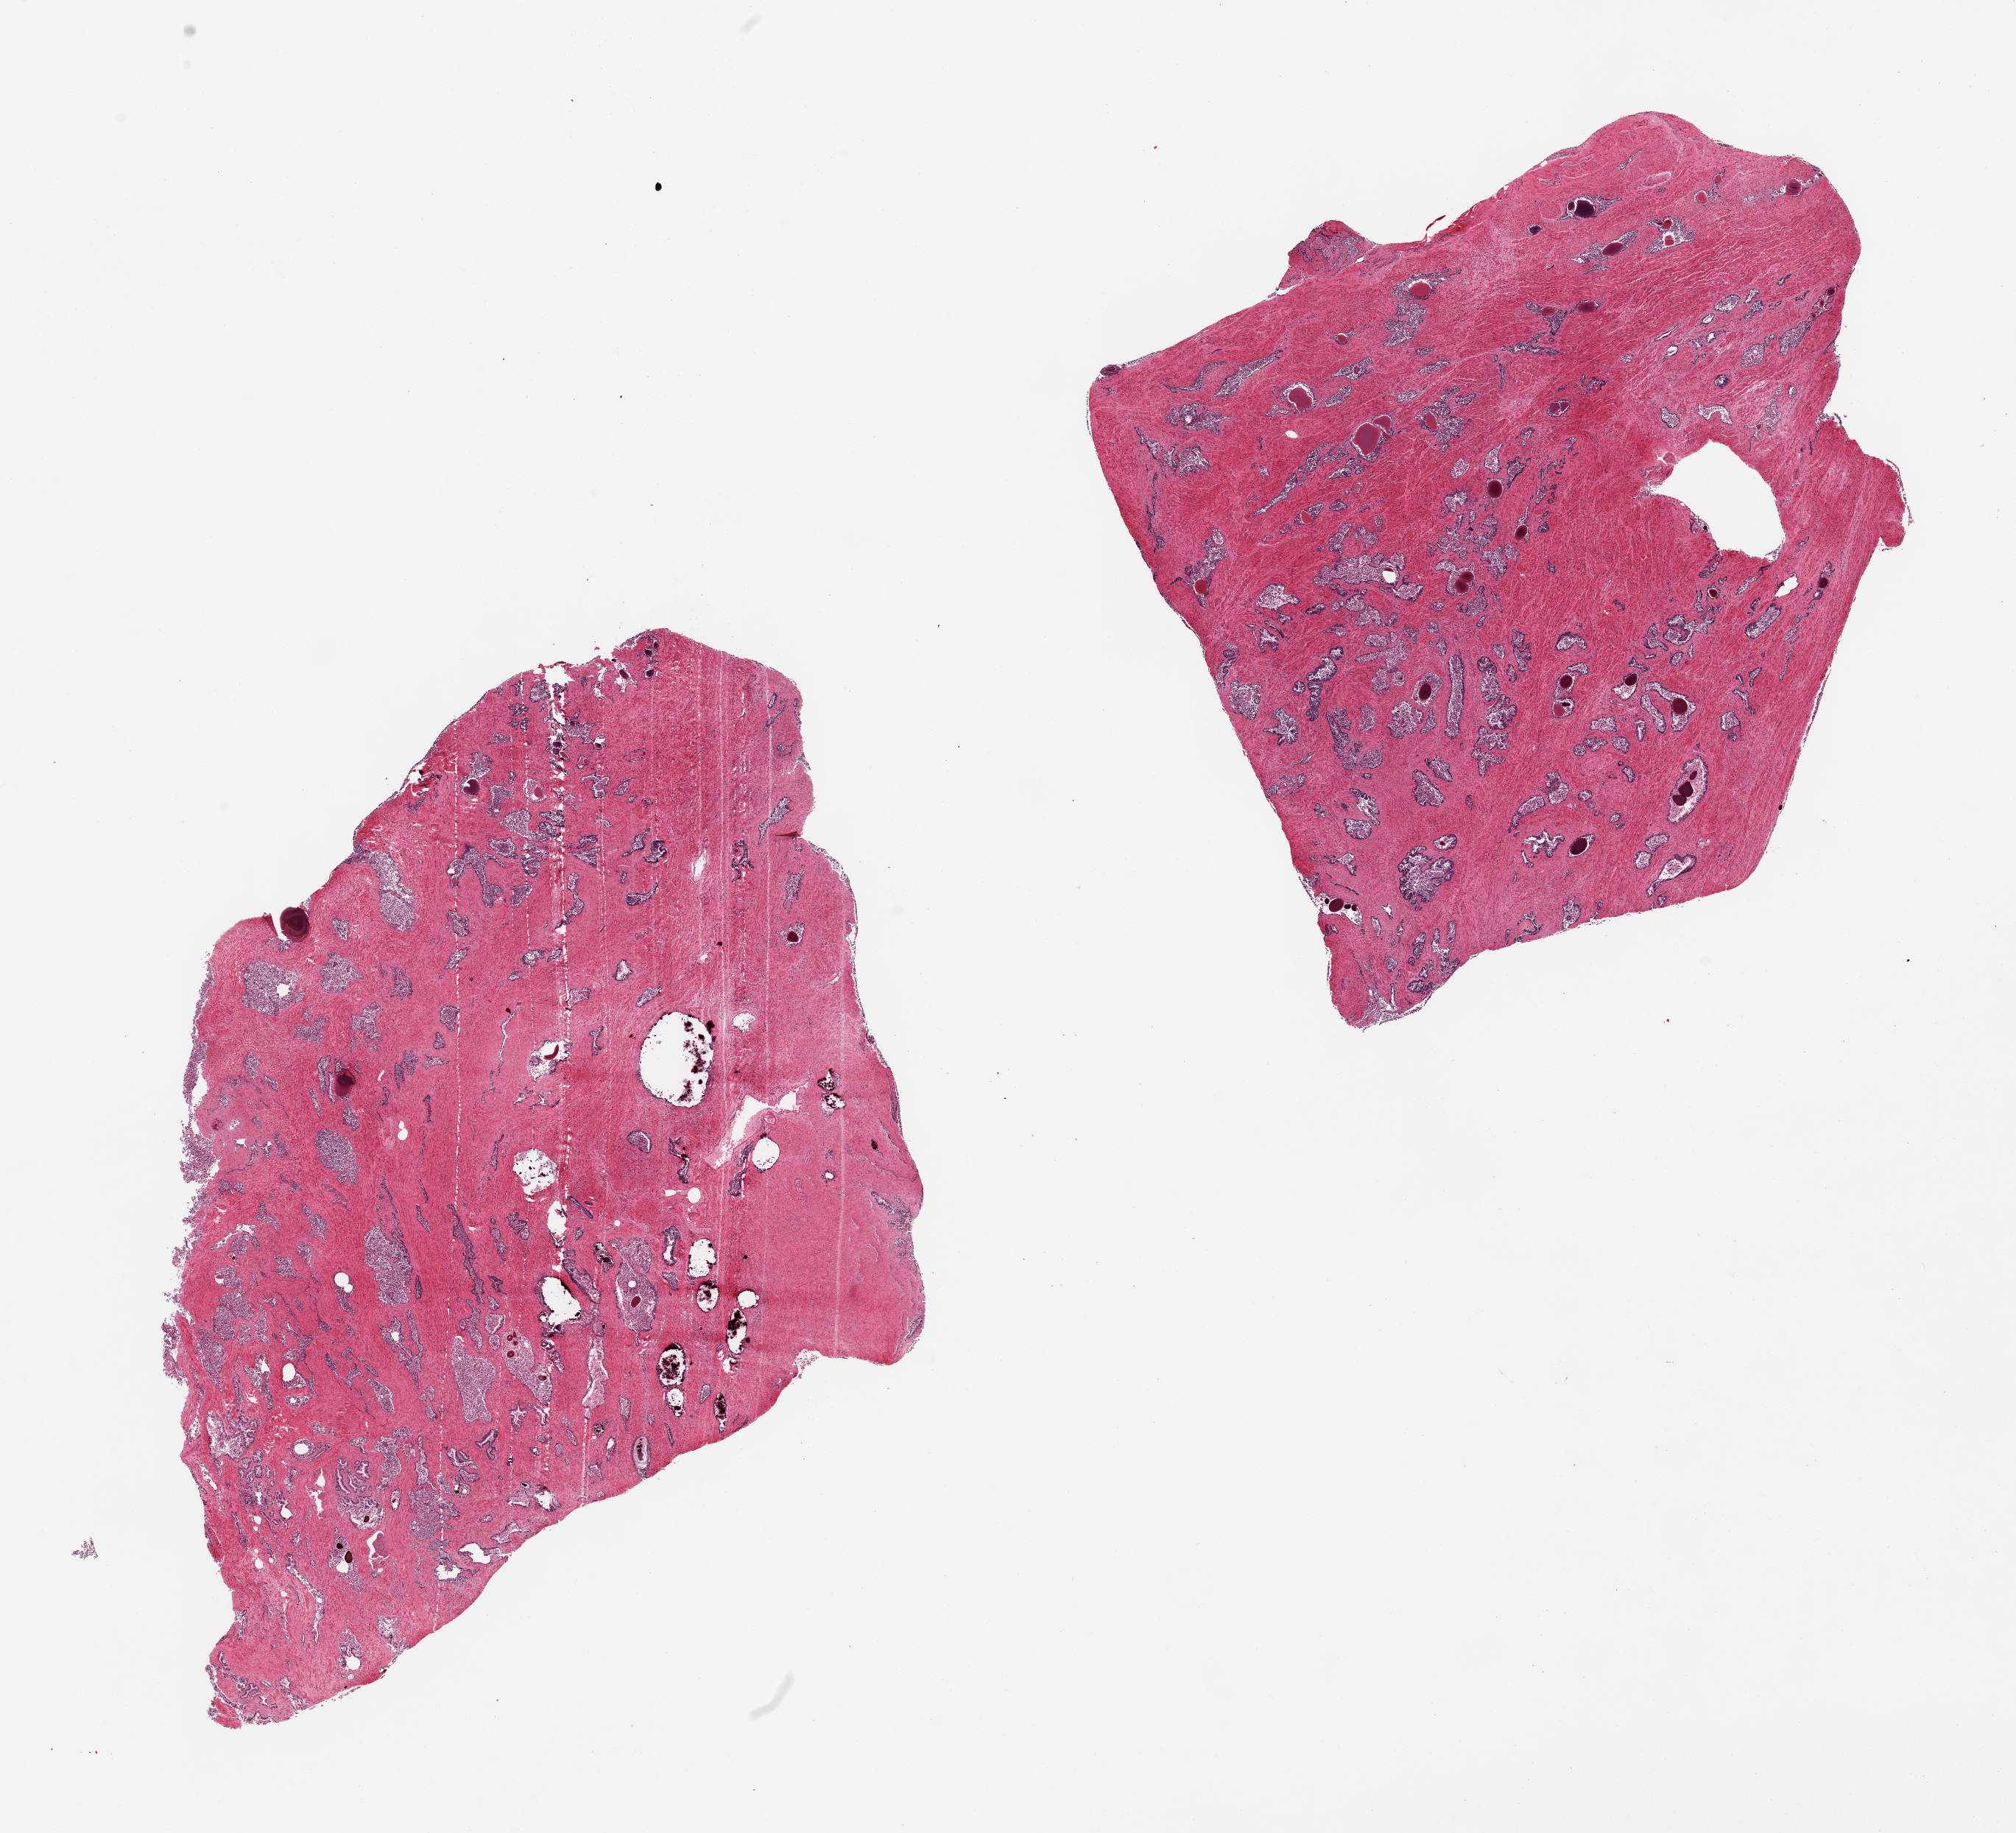
Digitized H&E-stained section, brightfield — a low-resolution overview of the entire scanned area, about 21.7 x 19.7 mm. PAXgene-fixed, paraffin-embedded tissue. Target tissue: prostate. Donor tissue sample. Donor: male.
Pathologist's review note for this sample: 2 pieces. Glands autolyzed; stroma preserved.